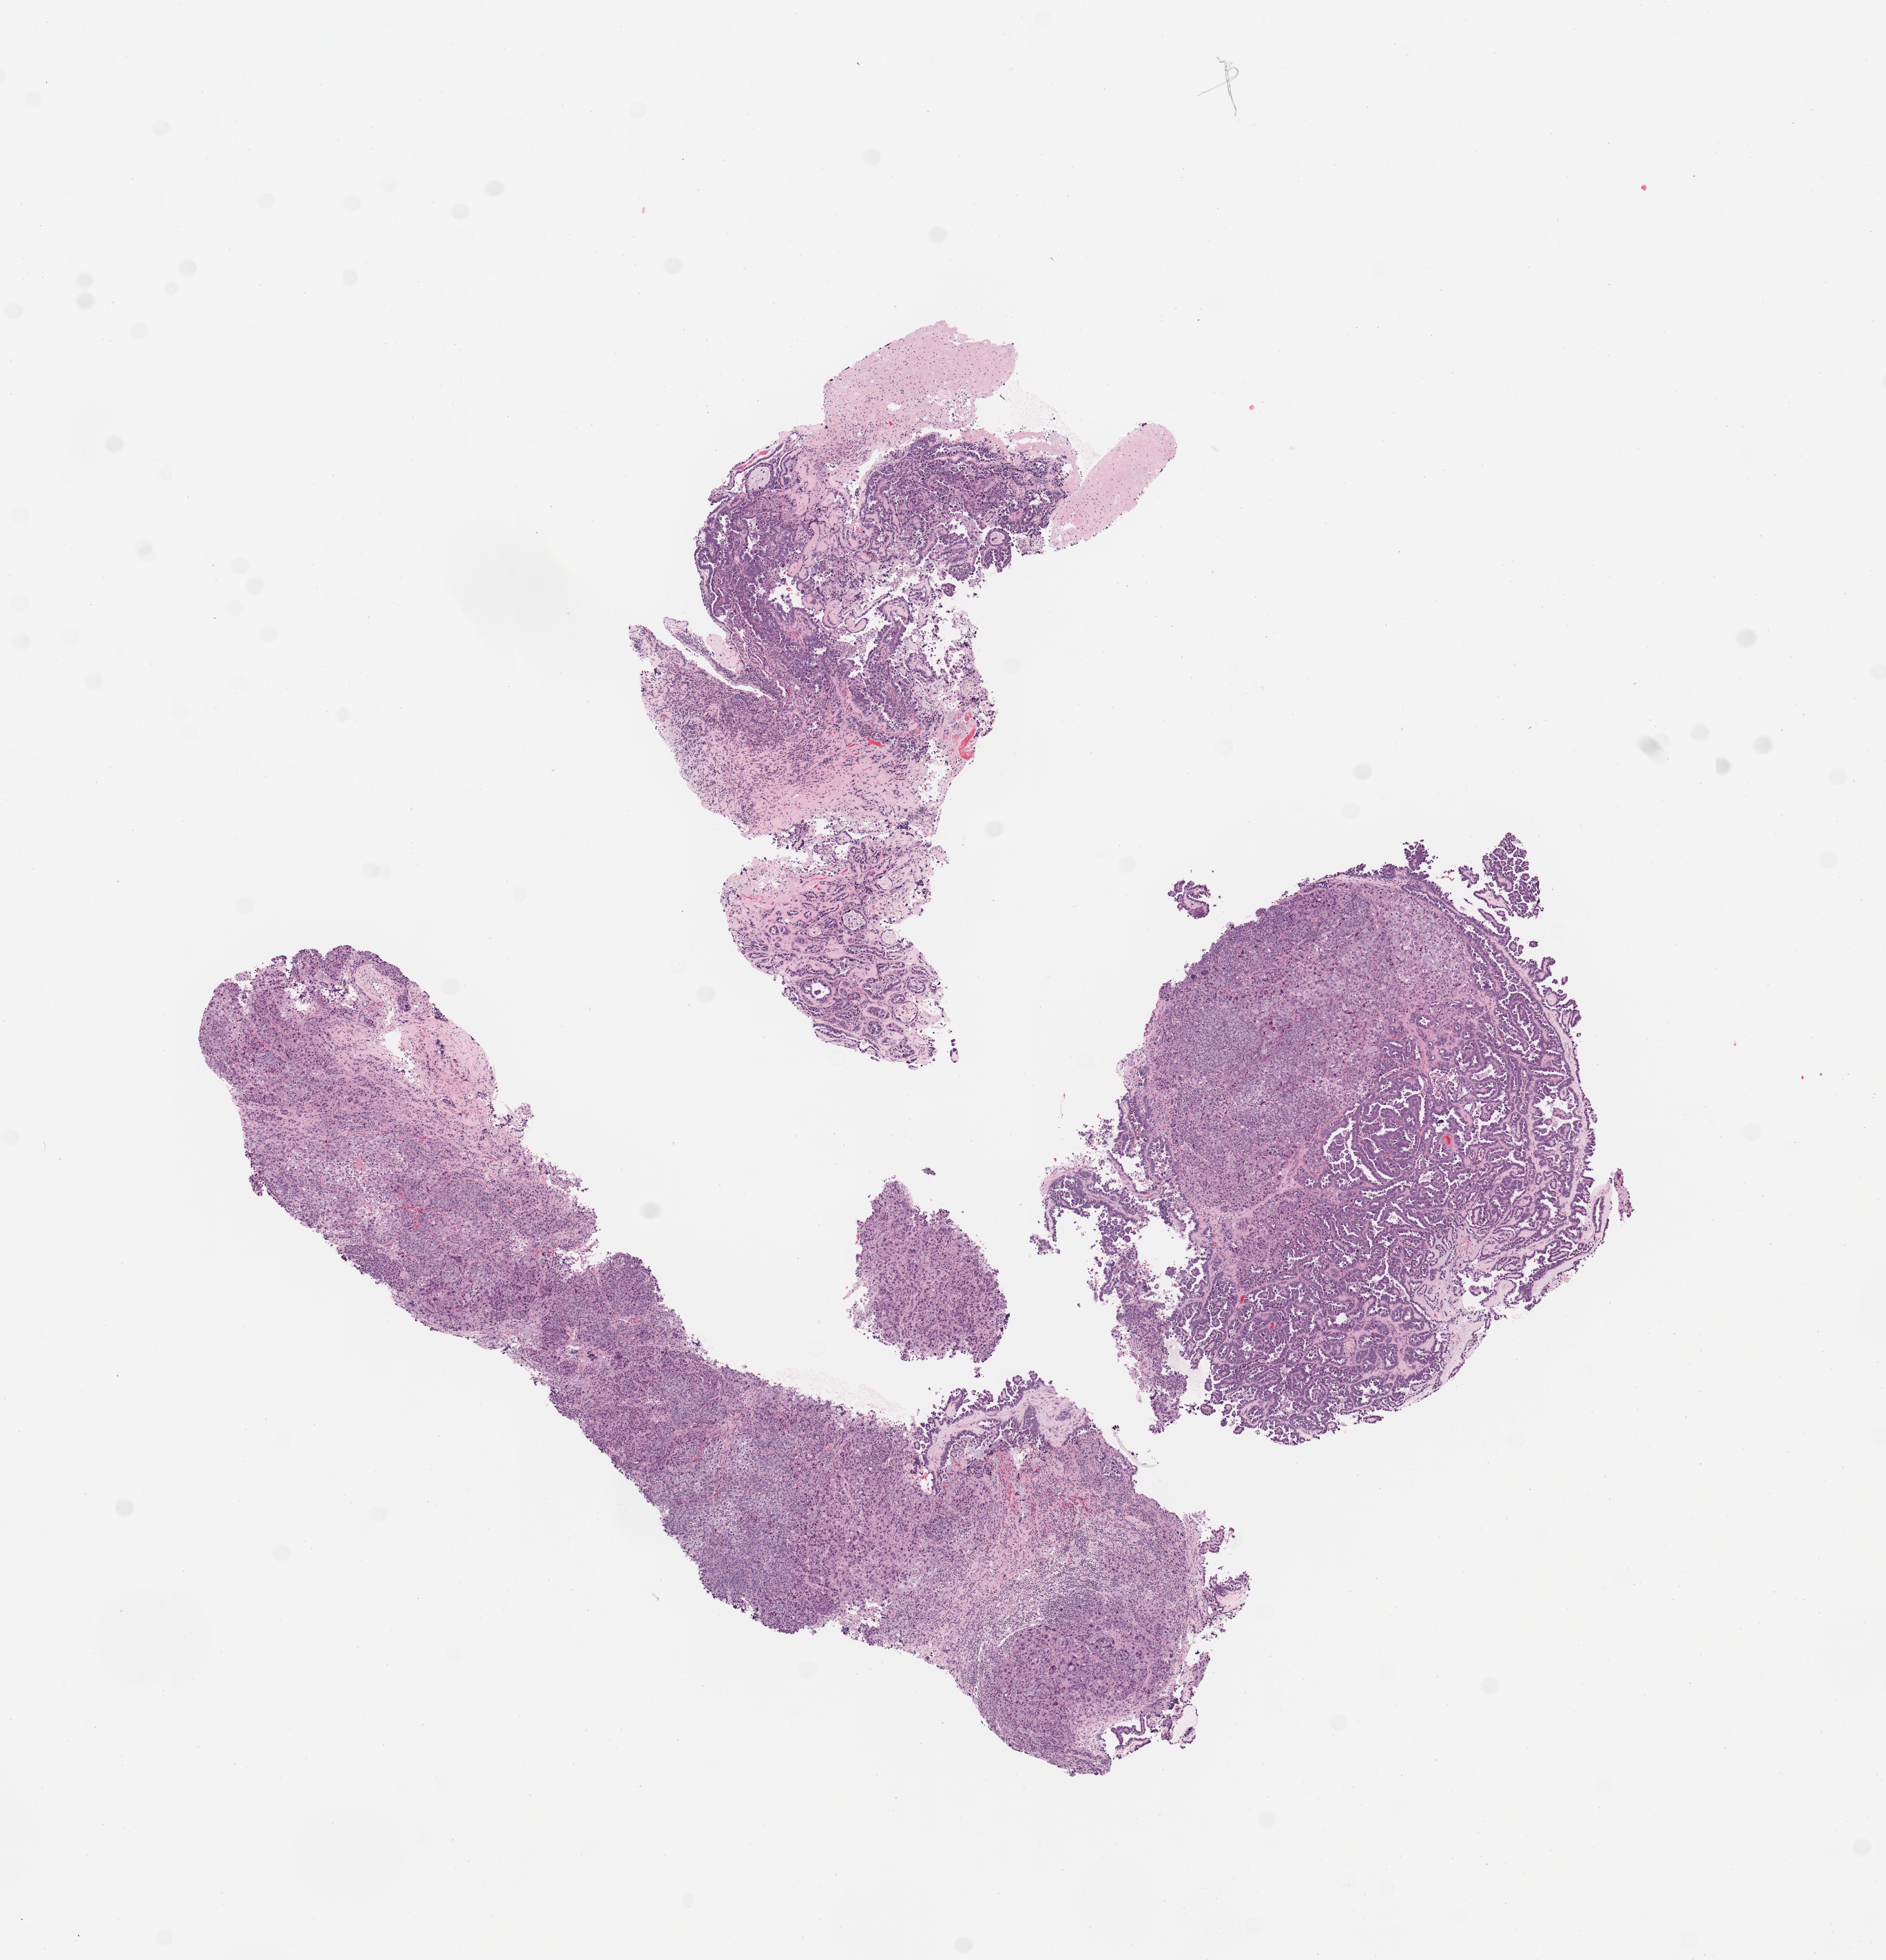
H&E-stained whole-slide image — low-resolution overview of the scanned area, about 10.8 x 11.3 mm (from a 20x scan), tumour tissue sample, sampled site: uterus. Patient: female, age 63 years. Histologic grade: G3 (poorly differentiated). Composition of this section per pathologist review: tumour nuclei 95%, necrosis 2%.
AJCC pathologic stage: I. Diagnosis: Endometrioid adenocarcinoma, NOS.